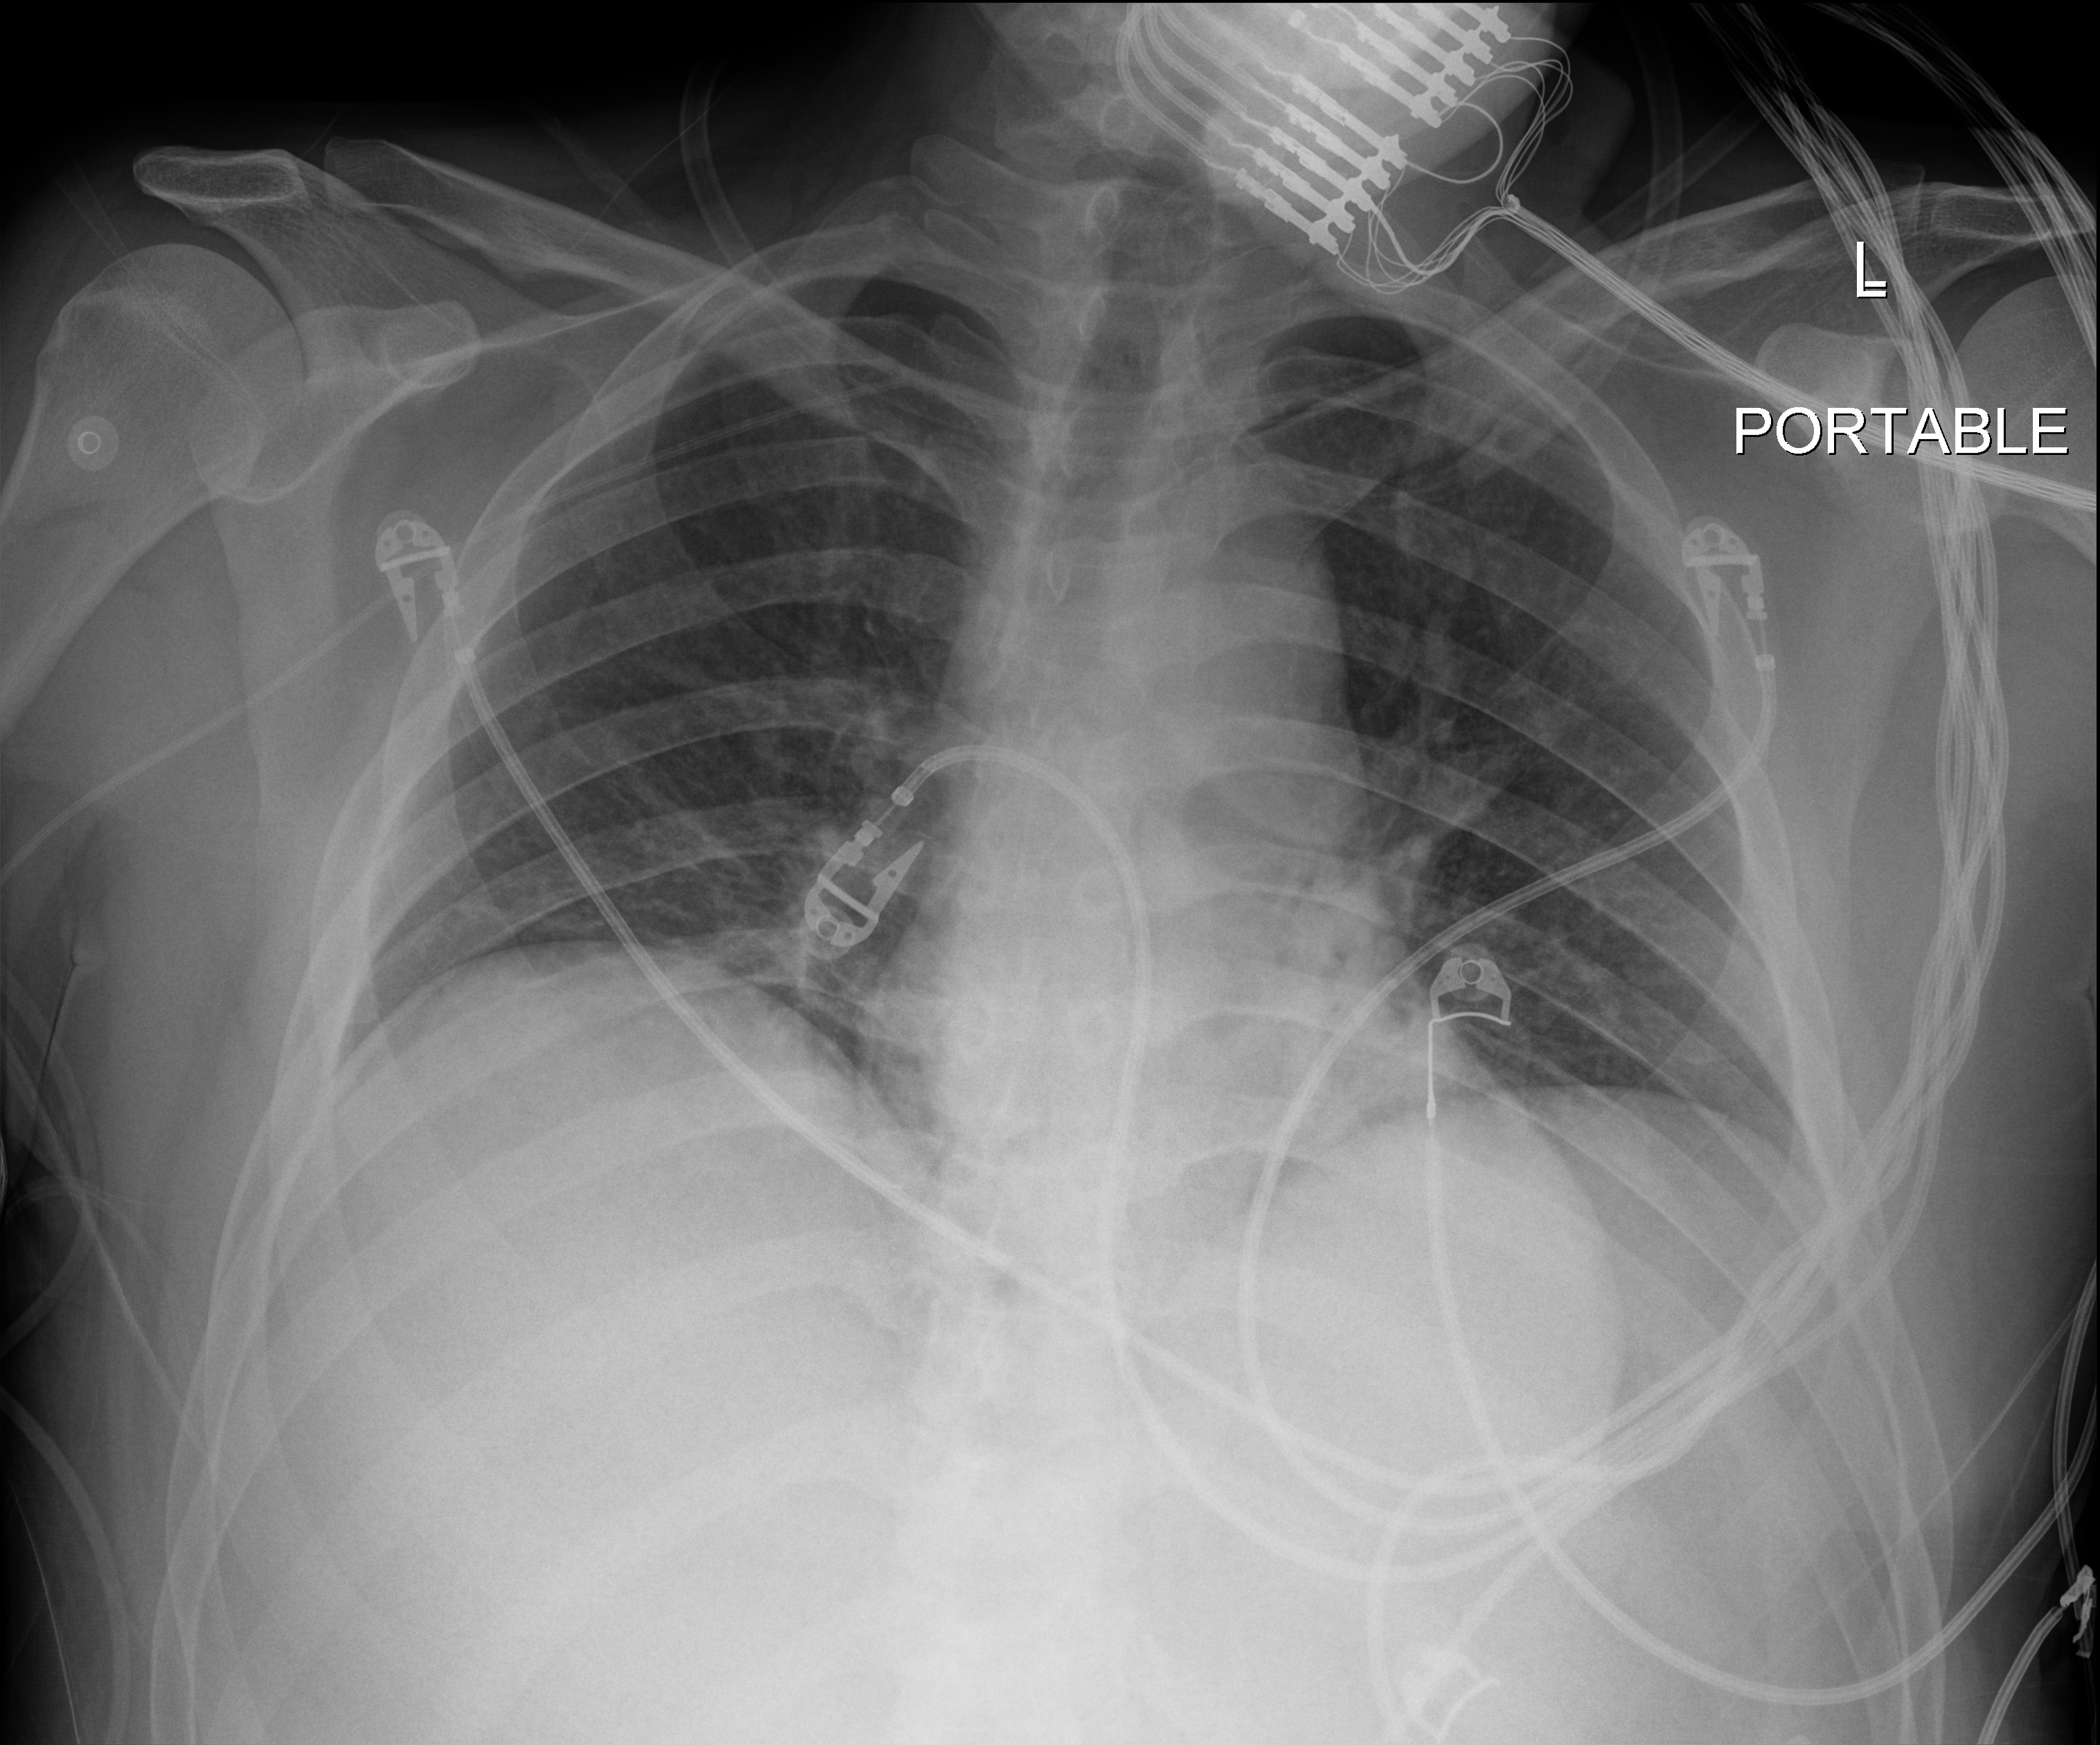
Portable chest radiograph, anteroposterior (AP) projection. Male patient hospitalised with COVID-19, age 18–59 years.
Admission-level facts for this patient (not findings on this image; timing relative to this image not recorded):
- admitted to intensive care during this hospital stay: yes
- chronic kidney disease (admission record): no